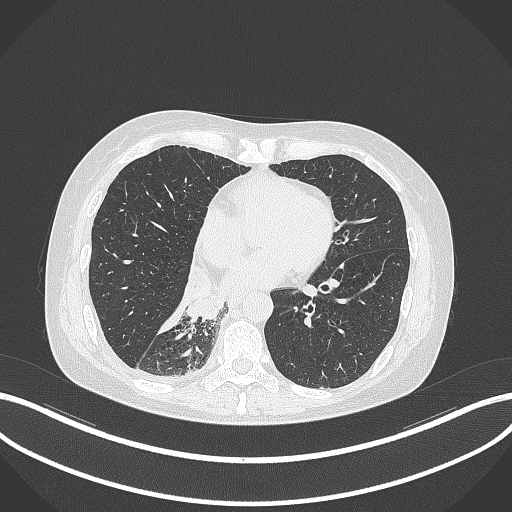
Chest CT, one axial slice. Reconstruction kernel B70f. Lung window (W 1500 / L -600 HU). 1 mm slice thickness. 512 × 512 image matrix, field of view 400 × 400 mm. Patient: female, 63 years. From the clinical record (not read from this slice): clinical TNM (as recorded): T1c N0 M0.
Annotated regions visible in this slice (bounding box drawn by a radiologist):
- lung tumour (recorded histology: adenocarcinoma): box from (x=177, y=269) to (x=219, y=321) px